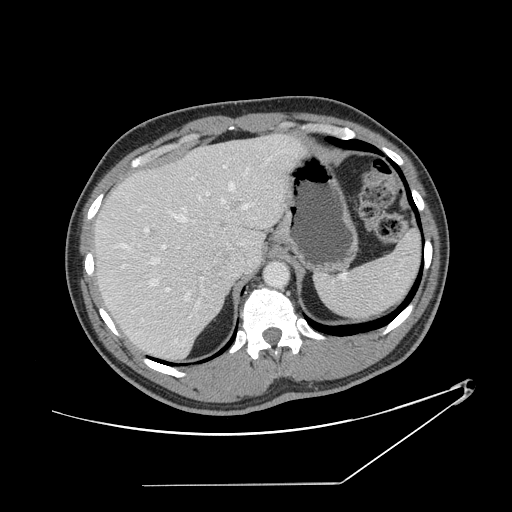
Contrast-enhanced abdominal CT, one axial slice. Reconstruction kernel STANDARD. Intravenous contrast given. Soft-tissue window (W 400 / L 40 HU). 512 × 512 image matrix, field of view 432 × 432 mm. Male patient, age 45 years. From the clinical record (not read from this slice): diagnosis: colorectal cancer liver metastases, imaged before liver resection; multiple liver metastases: no; largest metastasis: 1 cm; disease in both lobes: no.
Outlined on this slice (manually delineated by an expert):
- hepatic veins: bounding box (x1, y1, x2, y2) in pixels: (111, 158, 271, 300)
- liver: (96, 135, 300, 362)
- planned liver remnant (the part of the liver to remain after resection): (96, 155, 234, 361)
- portal vein (with intrahepatic branches): (162, 192, 249, 319)